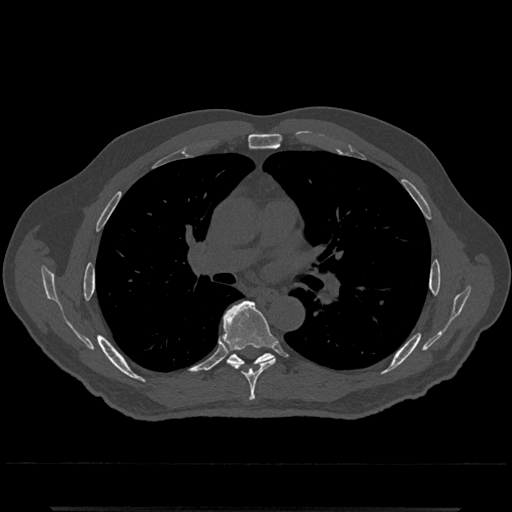
CT including the spine, one axial slice; position 754 of 797 along the scan axis; bone window (W 1800 / L 400 HU); 0.5 mm slice thickness; 512 × 512 image matrix, field of view 393 × 393 mm. Male patient, age 67 years. Case-level facts recorded for this patient, not image findings: primary cancer: prostate.
Annotated regions visible in this slice (semi-automatically segmented with operator editing):
- T6 vertebra: box from (x=222, y=300) to (x=276, y=401) px
- T7 vertebra: (x=228, y=352)–(x=274, y=367)